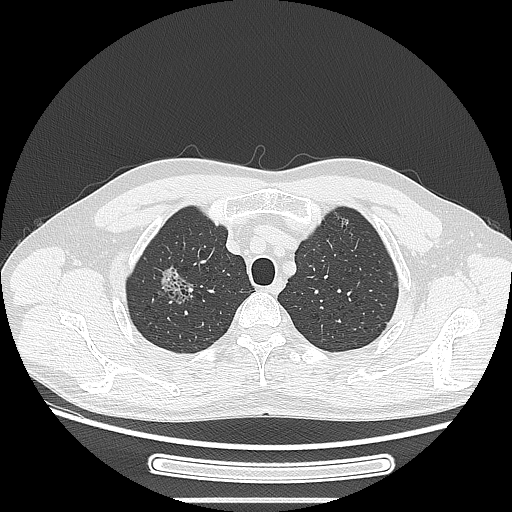
Chest CT, one axial slice. Position 221 of 269 along the scan axis. 120 kVp. Lung window (W 1500 / L -600 HU). 1.25 mm slice thickness. 512 × 512 image matrix, field of view 382 × 382 mm. Patient: male, 53 years. Case-level facts recorded for this patient, not image findings: clinical TNM (as recorded): T1c N0 M0; histopathological grade: G2.
Annotated regions visible in this slice (bounding box drawn by a radiologist):
- lung tumour (recorded histology: adenocarcinoma): bounding box (x1, y1, x2, y2) in pixels: (144, 250, 195, 314)